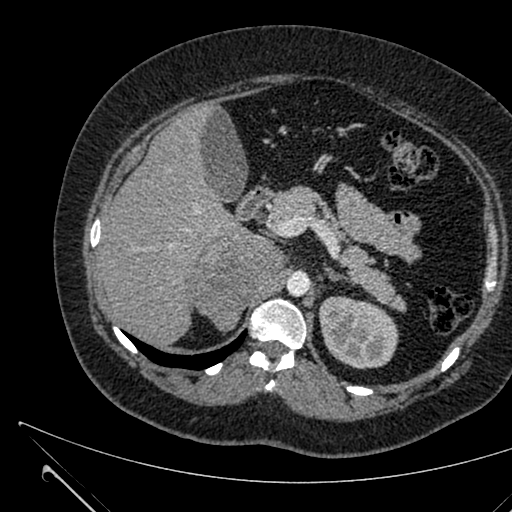
Contrast-enhanced abdominal CT, one axial slice. Slice 427 of 731 in the series (ordered by position). Intravenous contrast given. Soft-tissue window (W 400 / L 40 HU). 1 mm slice thickness. 512 × 512 image matrix. Patient: female, 36 years. From the clinical record (not read from this slice): diagnosis: adrenocortical carcinoma; tumour side: right adrenal; tumour size at pathology: 10 cm; Ki-67 index: 20 %; stage (as recorded): 4.
Outlined on this slice (semi-automatic segmentation, software-assisted and operator-edited):
- mass: bounding box <194,237,285,331> (left, top, right, bottom; pixels)